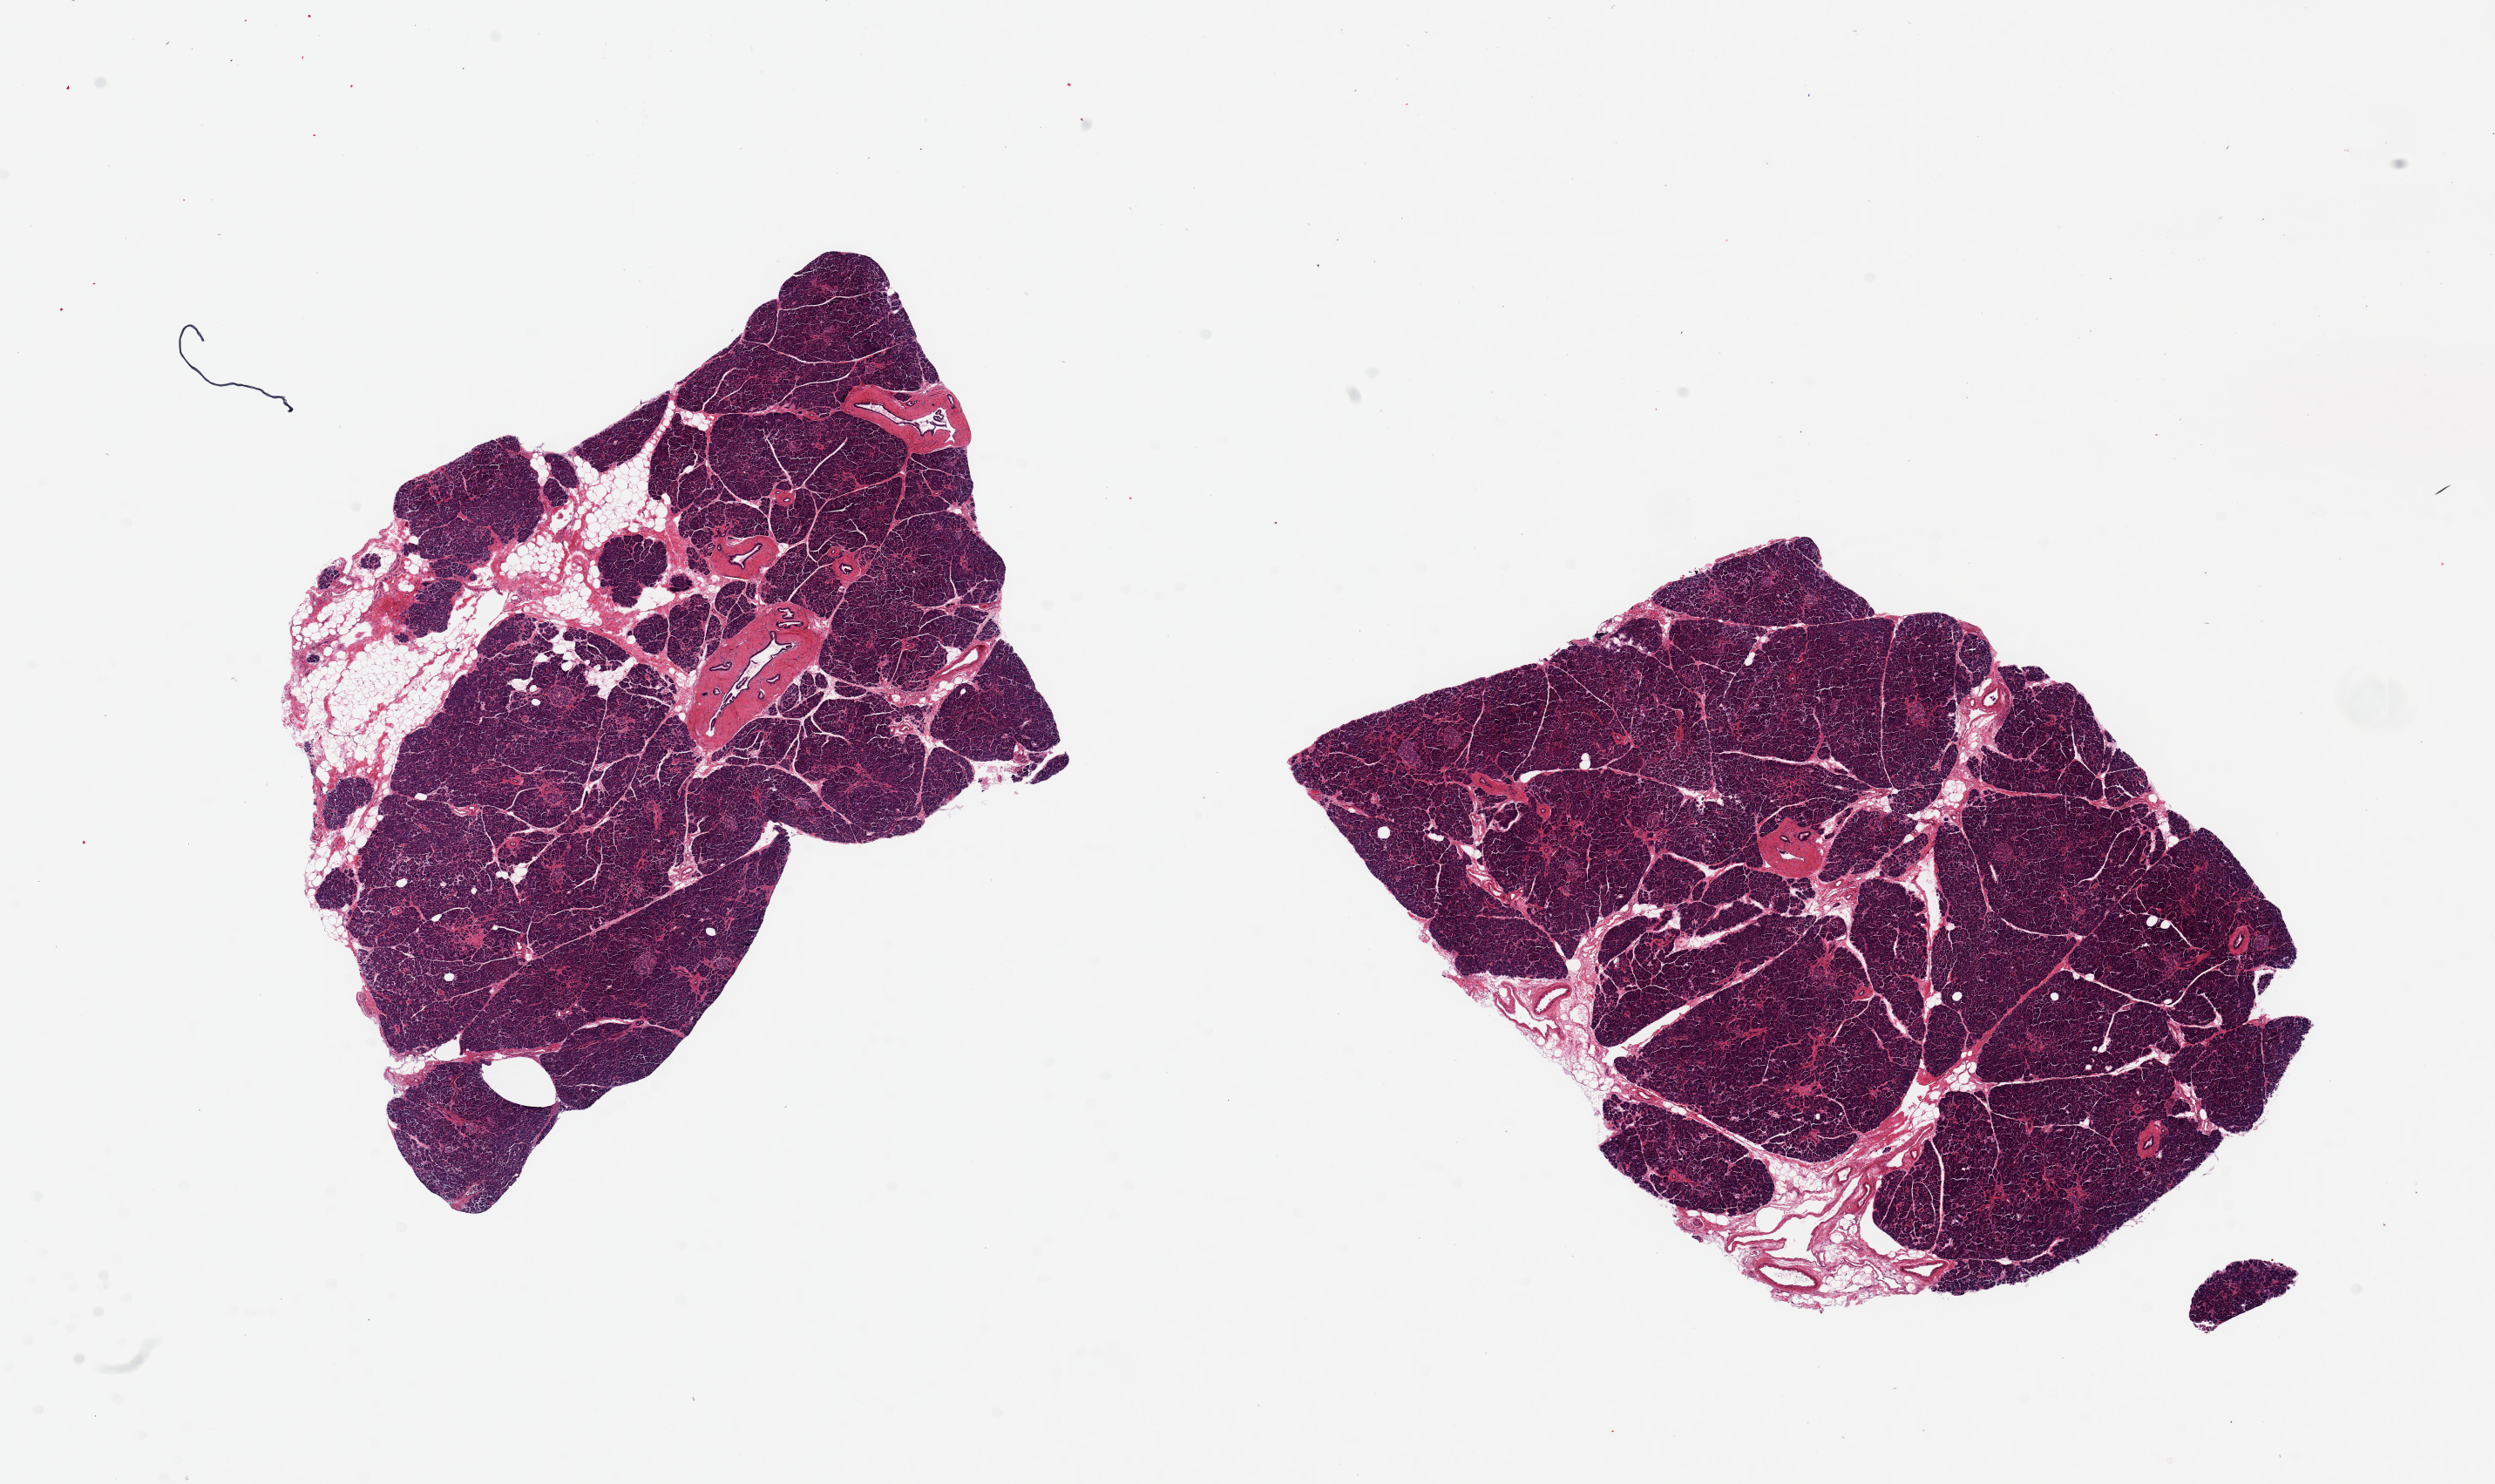
Whole-slide image, haematoxylin and eosin stain, shown as a low-resolution overview of the whole scanned area (about 22.6 x 13.5 mm, slide scanned at 20x). PAXgene-fixed paraffin-embedded (PFPE) section. Target tissue: pancreas. Donor tissue sample. Donor: male.
* reviewer comment on this tissue sample: 2 pieces, 7x6 & 8x6mm; ~10% internal adipose; good islets